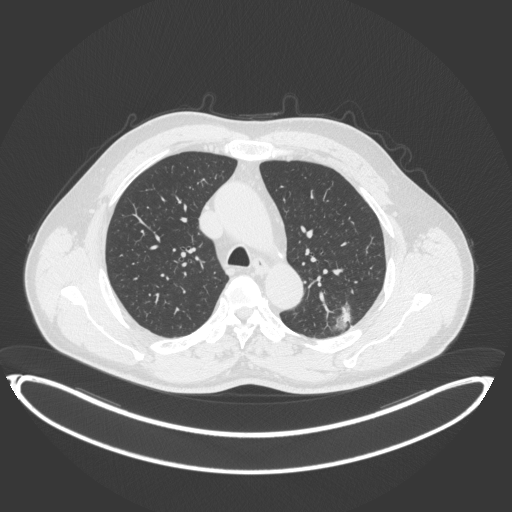
Chest CT, one axial slice. Position 254 of 399 along the scan axis. 120 kVp. Lung window (W 1500 / L -600 HU). 1 mm slice thickness. 512 × 512 image matrix, field of view 469 × 469 mm. Male patient, age 58 years. Case-level facts recorded for this patient, not image findings: clinical TNM (as recorded): T1c N0 M0; histopathological grade: G1-2.
Outlined on this slice (bounding box drawn by a radiologist):
- lung tumour (recorded histology: adenocarcinoma): box from (x=331, y=296) to (x=357, y=333) px